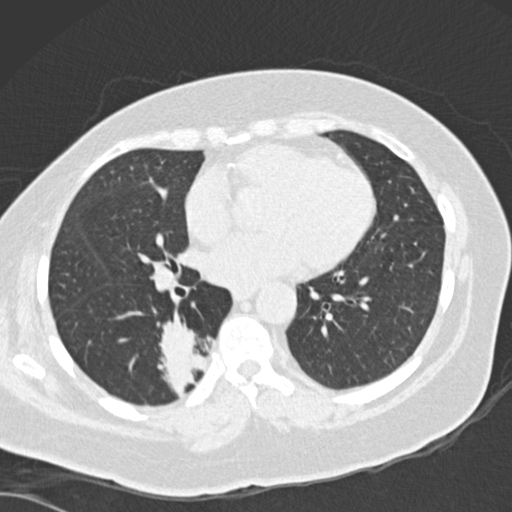
Low-dose screening chest CT, axial slice. First (baseline) screen. Lung window (W 1500 / L -600 HU). Standard (soft-tissue) reconstruction kernel (B30f). 120 kVp. Slice 93 of 162 in the series. 512 × 512 image matrix, field of view 328 × 328 mm. Female, age 66 years at enrolment.
- Expert reader's lesion annotation, box from (x=151, y=322) to (x=225, y=398) px.
- The screening reader recorded 3 non-calcified nodules or masses ≥4 mm on this exam (left lower lobe, left lower lobe, right lower lobe); which of them this box marks is not recorded.
- Official screen result: positive, change unspecified: nodule(s) >= 4 mm or enlarging nodule(s), mass(es), or other non-specific abnormalities suspicious for lung cancer.
- Lung cancer was diagnosed 67 days after this screen: adenocarcinoma, NOS, right lower lobe, well differentiated (G1), stage IB (AJCC 6th edition), 55 mm at pathology.